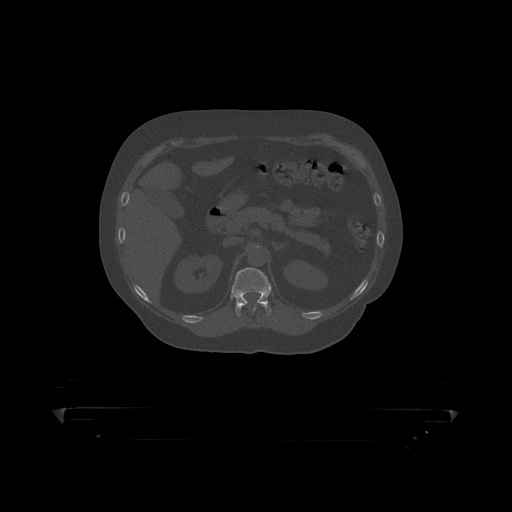
CT including the spine, one axial slice; slice 179 of 390 in the series (ordered by position); reconstruction kernel STANDARD; 120 kVp; bone window (W 1800 / L 400 HU); 1.25 mm slice thickness; 512 × 512 image matrix, field of view 650 × 650 mm. Male patient, age 60 years. Case-level facts recorded for this patient, not image findings: primary cancer: prostate.
Structures marked on this image (semi-automatic segmentation, software-assisted and operator-edited):
- T11 vertebra: bounding box [x1, y1, x2, y2] px = [253, 304, 267, 313]
- T12 vertebra: [232, 268, 272, 317]